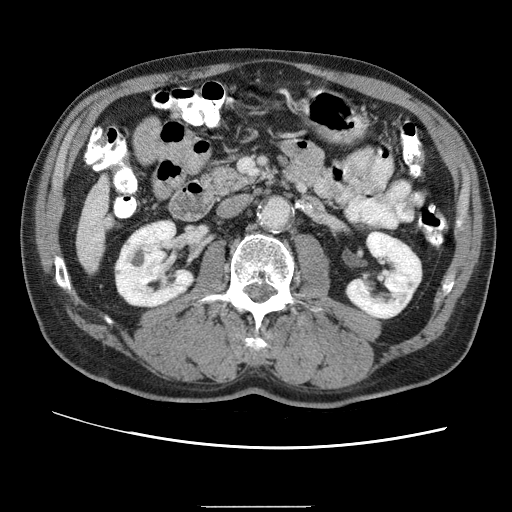
Contrast-enhanced abdominal CT (liver protocol), one axial slice. Position 6 of 75 along the scan axis. Reconstruction kernel STANDARD. One of 2 acquisitions stored at this slice position. Soft-tissue window (W 400 / L 40 HU). 2.5 mm slice thickness. 512 × 512 image matrix. From the clinical record (not read from this slice): diagnosis: hepatocellular carcinoma (patient treated with transarterial chemoembolisation; whether this scan precedes or follows treatment is not stated here); TNM stage (as recorded): Stage-II; Child-Pugh class: A.
Structures marked on this image (semi-automatic segmentation, software-assisted and operator-edited):
- liver parenchyma outside the tumour (the mass and vessels are separate outlines, so this box may not span the whole liver): box from (x=78, y=188) to (x=100, y=258) px
- liver vessels: (x=83, y=193)–(x=98, y=250)